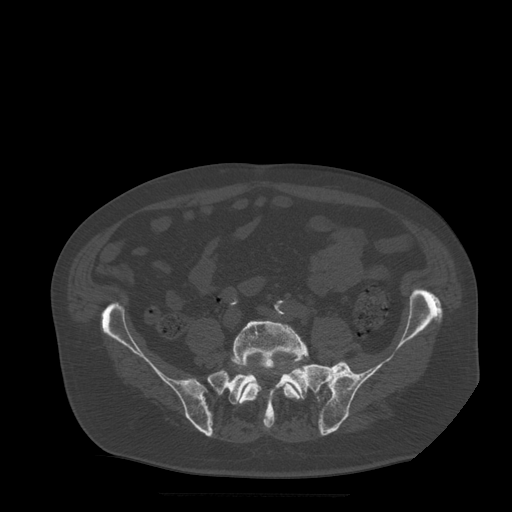
CT including the spine, one axial slice. Slice 79 of 522 in the series (ordered by position). Bone window (W 1800 / L 400 HU). 1.25 mm slice thickness. 512 × 512 image matrix. Patient age 72 years. Case-level facts recorded for this patient, not image findings: primary cancer: prostate.
Structures marked on this image (semi-automatic segmentation, software-assisted and operator-edited):
- L5 vertebra: bounding box <232,321,308,404> (left, top, right, bottom; pixels)